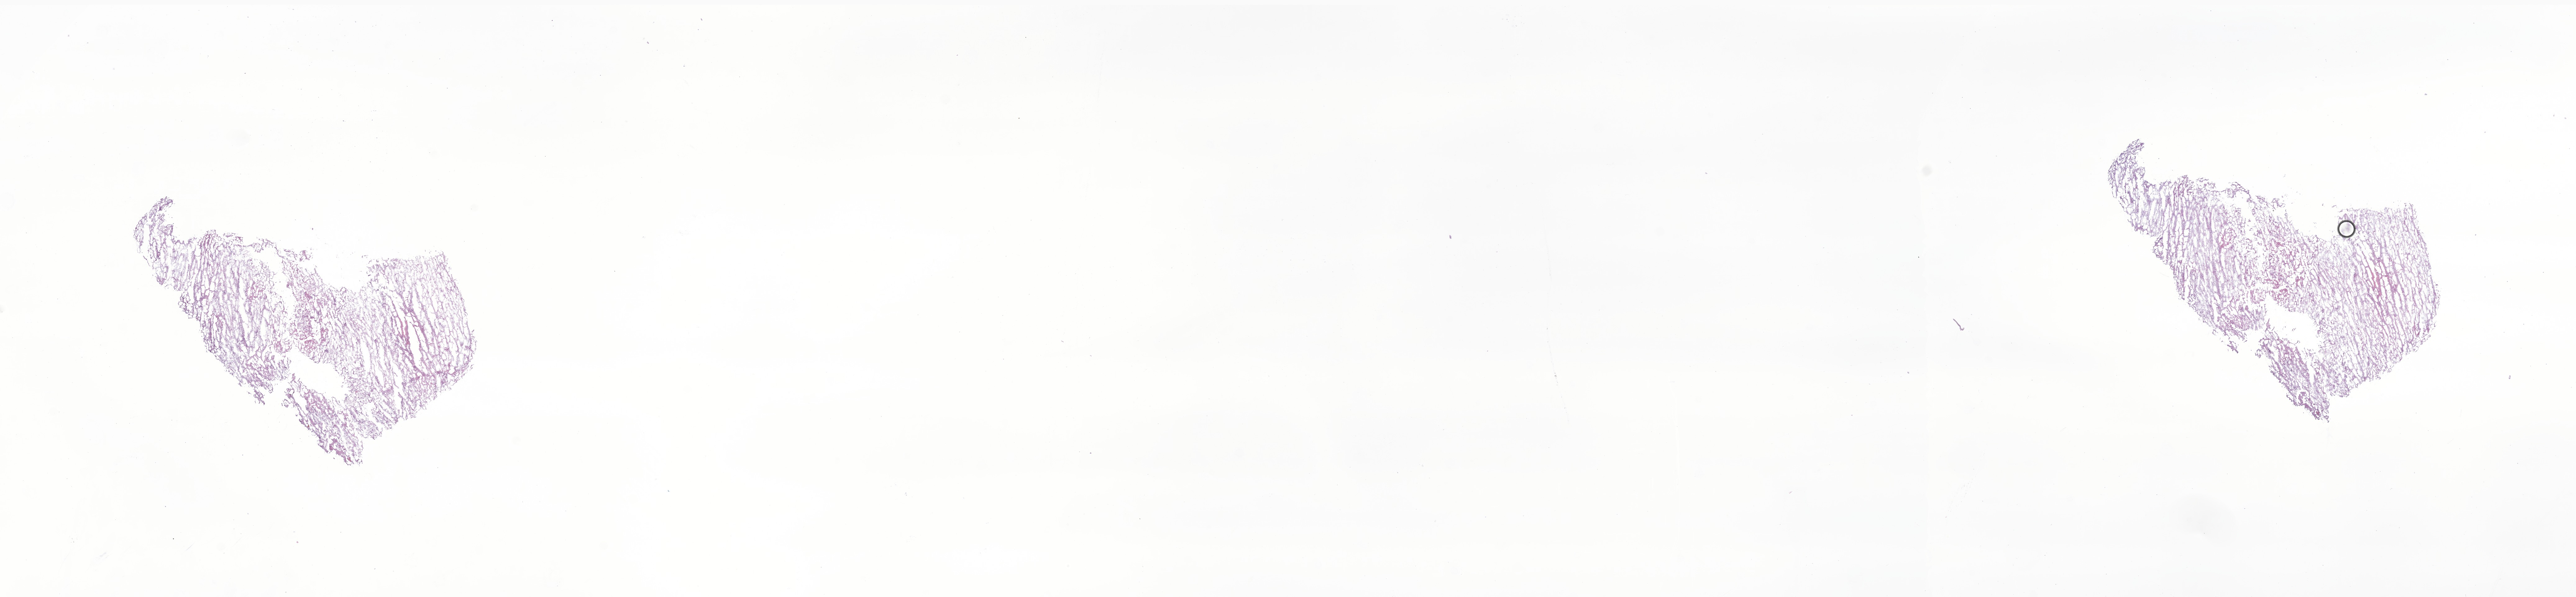
Hematoxylin and eosin (H&E) whole-slide image of tumor tissue from the brain, a low-resolution overview of the entire scanned area, about 35.0 x 8.1 mm. Frozen section. Patient female; age 203 months (16 years 11 months).
Diagnosis (ICD-O-3 morphology term): Pilocytic astrocytoma.